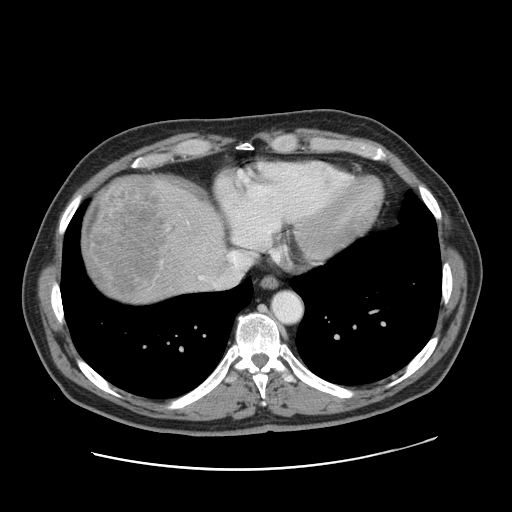
Contrast-enhanced abdominal CT, one axial slice; position 147 of 178 along the scan axis; 120 kVp; intravenous contrast given; soft-tissue window (W 400 / L 40 HU); 2.5 mm slice thickness; 512 × 512 image matrix, field of view 403 × 403 mm. Male patient, age 63 years. From the clinical record (not read from this slice): diagnosis: colorectal cancer liver metastases, imaged before liver resection; multiple liver metastases: yes; largest metastasis: 8 cm; chemotherapy before resection: no.
Outlined on this slice (manually delineated by an expert):
- hepatic veins: box from (x=200, y=251) to (x=251, y=287) px
- liver: (x=81, y=176)–(x=227, y=305)
- planned liver remnant (the part of the liver to remain after resection): (x=185, y=191)–(x=227, y=261)
- liver metastasis: (x=84, y=180)–(x=165, y=296)